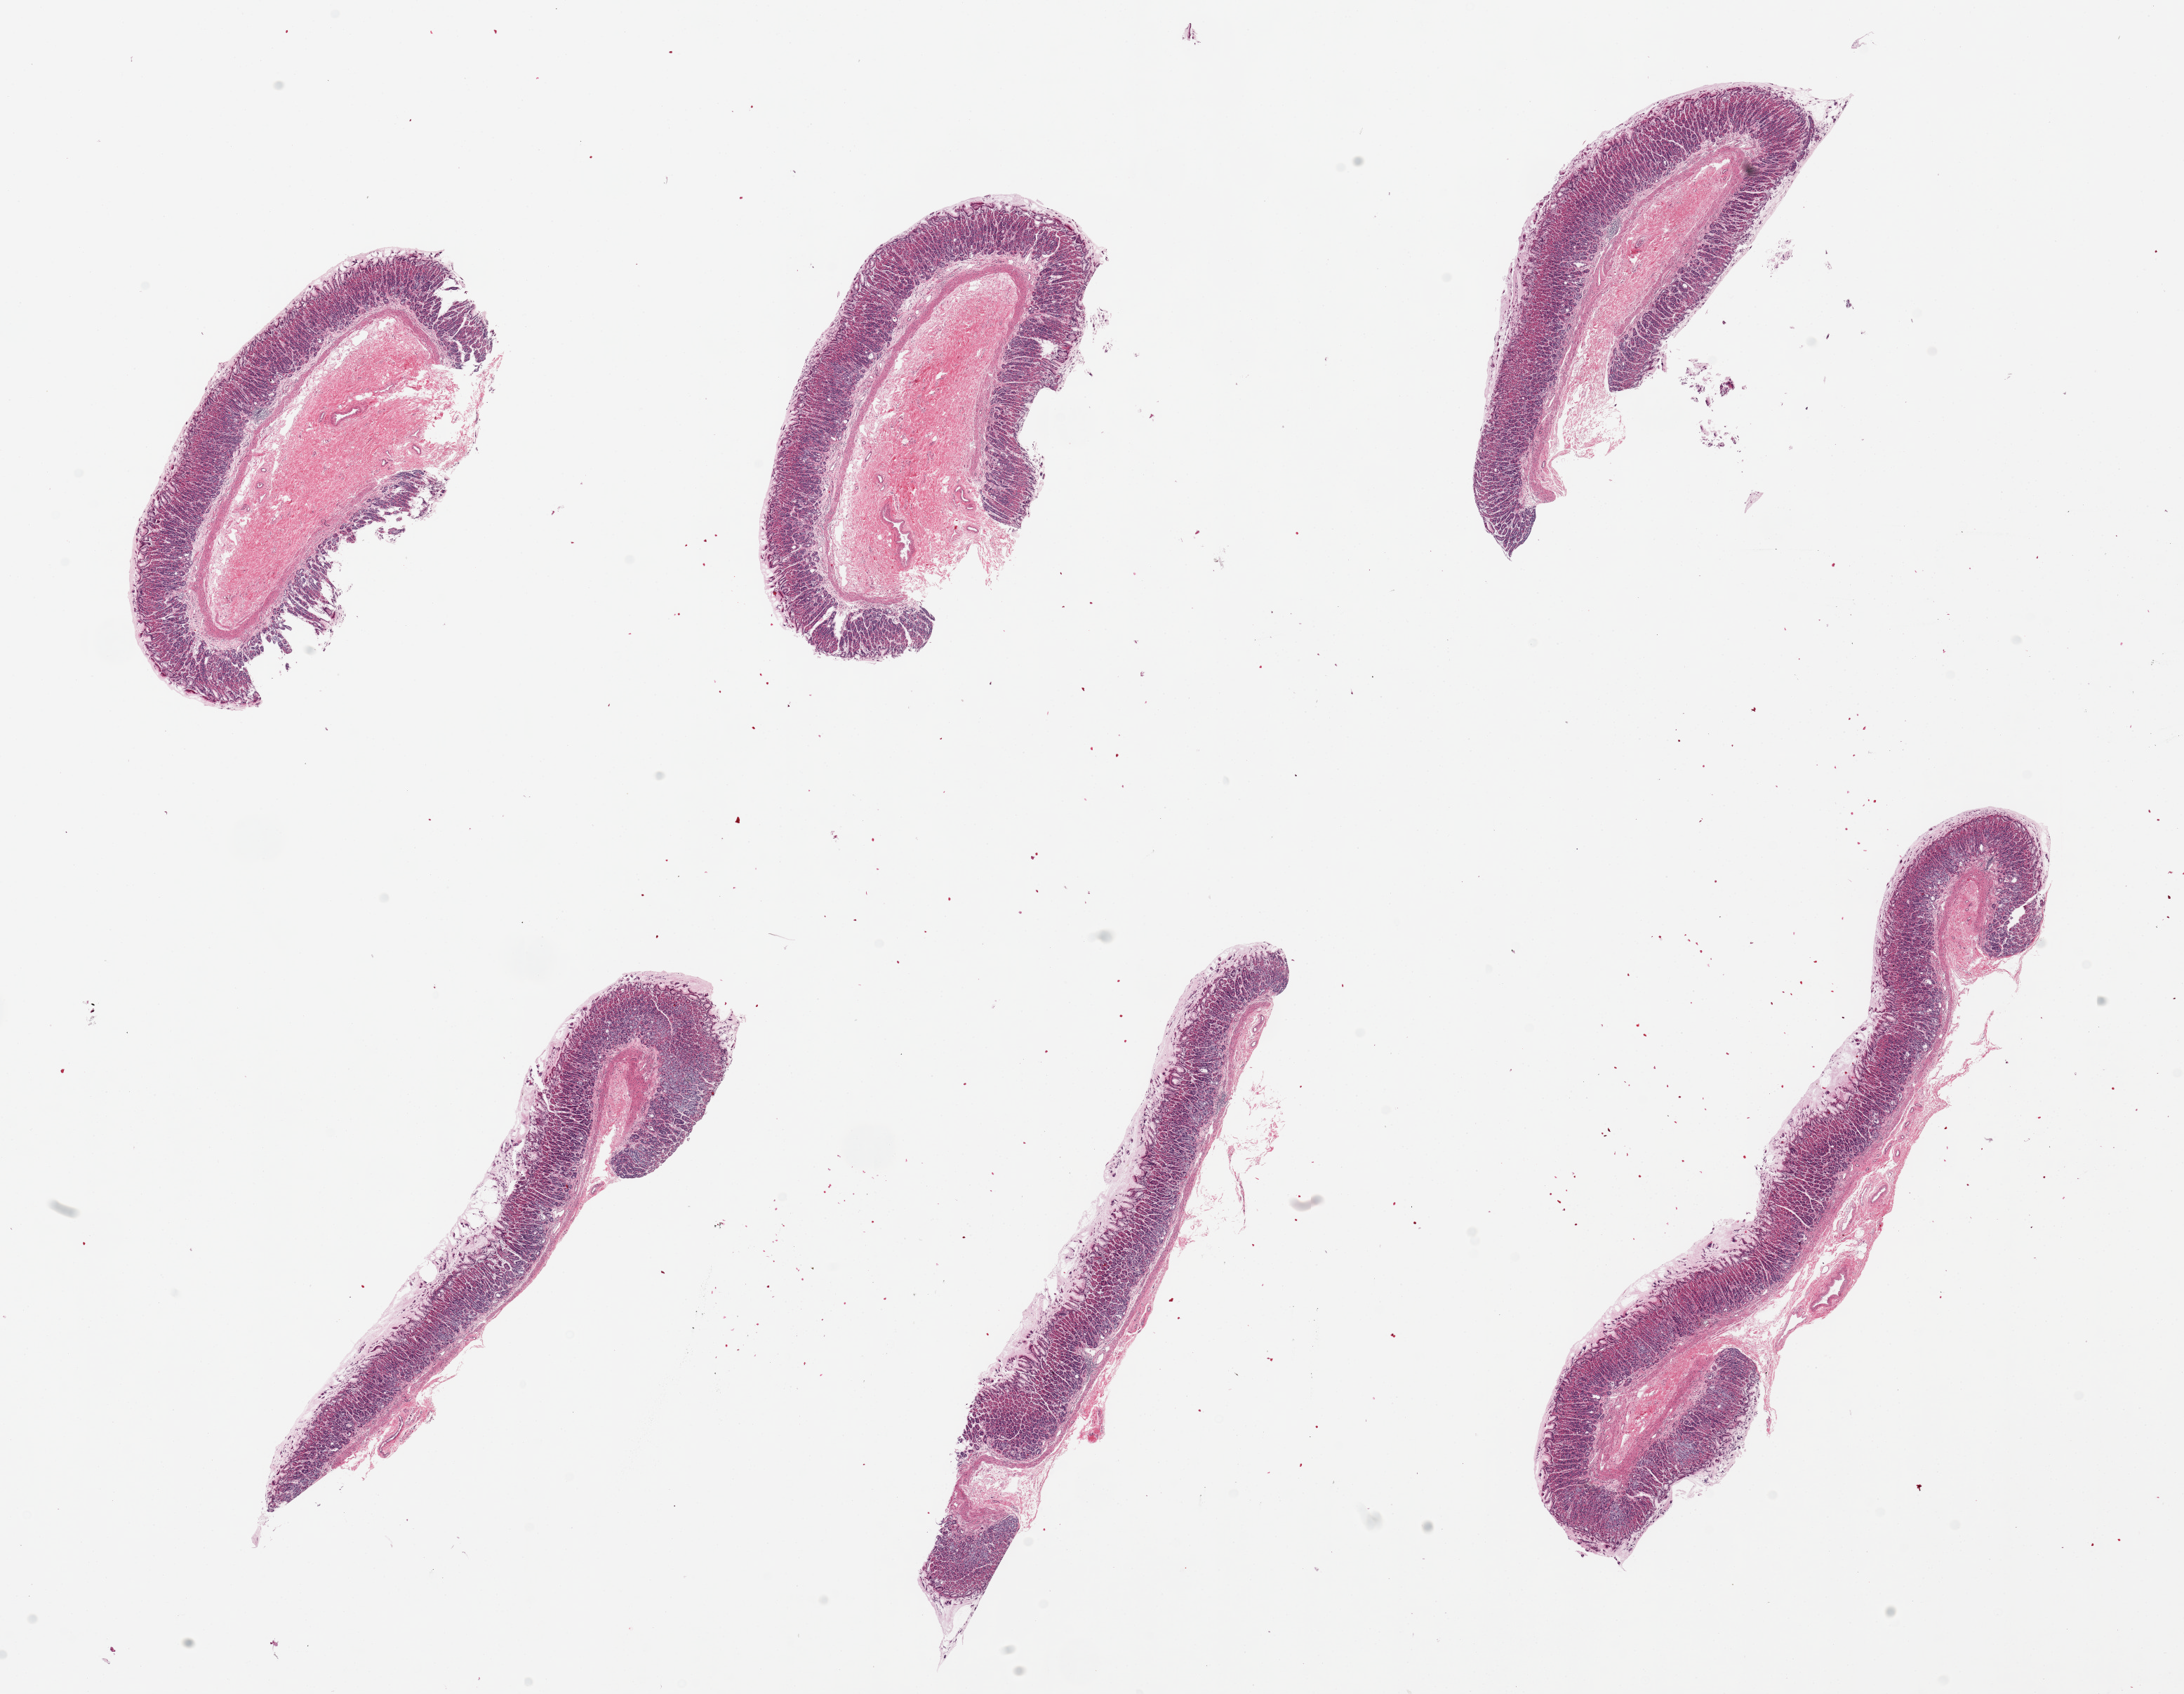
Whole-slide image, haematoxylin and eosin stain — a low-resolution overview of the entire scanned area, about 24.6 x 19.1 mm, PAXgene-fixed paraffin-embedded (PFPE) section, sampled site (target tissue): stomach, tissue donor sample.
Reviewer comment on this tissue sample: 6 pieces, all with mucosa.